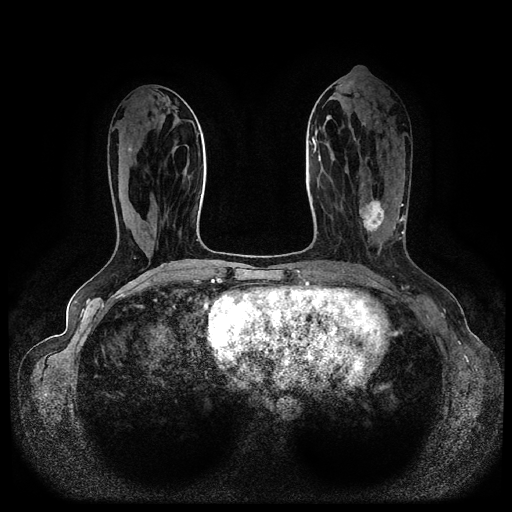
Breast MRI (dynamic contrast-enhanced, multi-phase), one axial slice. Slice 39 of 116 in the series (ordered by position). Dynamic contrast-enhanced series, time point 2 of 5 at this slice position (early post-contrast). 1.5 T. TE 2.6 ms, TR 5.3 ms. 2 mm slice thickness. 512 × 512 image matrix, field of view 350 × 350 mm. Patient: female, 45 years.
Outlined on this slice (semi-automatically segmented with operator editing):
- breast lesion (labelled 'tumour' in the annotation; benign lesions carry a separate 'benign' label): bounding box <359,190,390,240> (left, top, right, bottom; pixels)